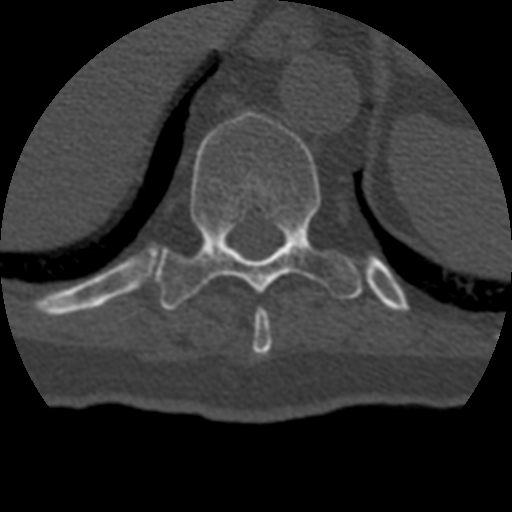
CT including the spine, one axial slice; position 220 of 399 along the scan axis; reconstruction kernel STANDARD; bone window (W 1800 / L 400 HU); 1.25 mm slice thickness; 512 × 512 image matrix, field of view 160 × 160 mm. Patient age 69 years. From the clinical record (not read from this slice): primary cancer: prostate.
Outlined on this slice (semi-automatically segmented with operator editing):
- T10 vertebra: box from (x=156, y=113) to (x=362, y=310) px
- T9 vertebra: (x=252, y=309)–(x=272, y=356)